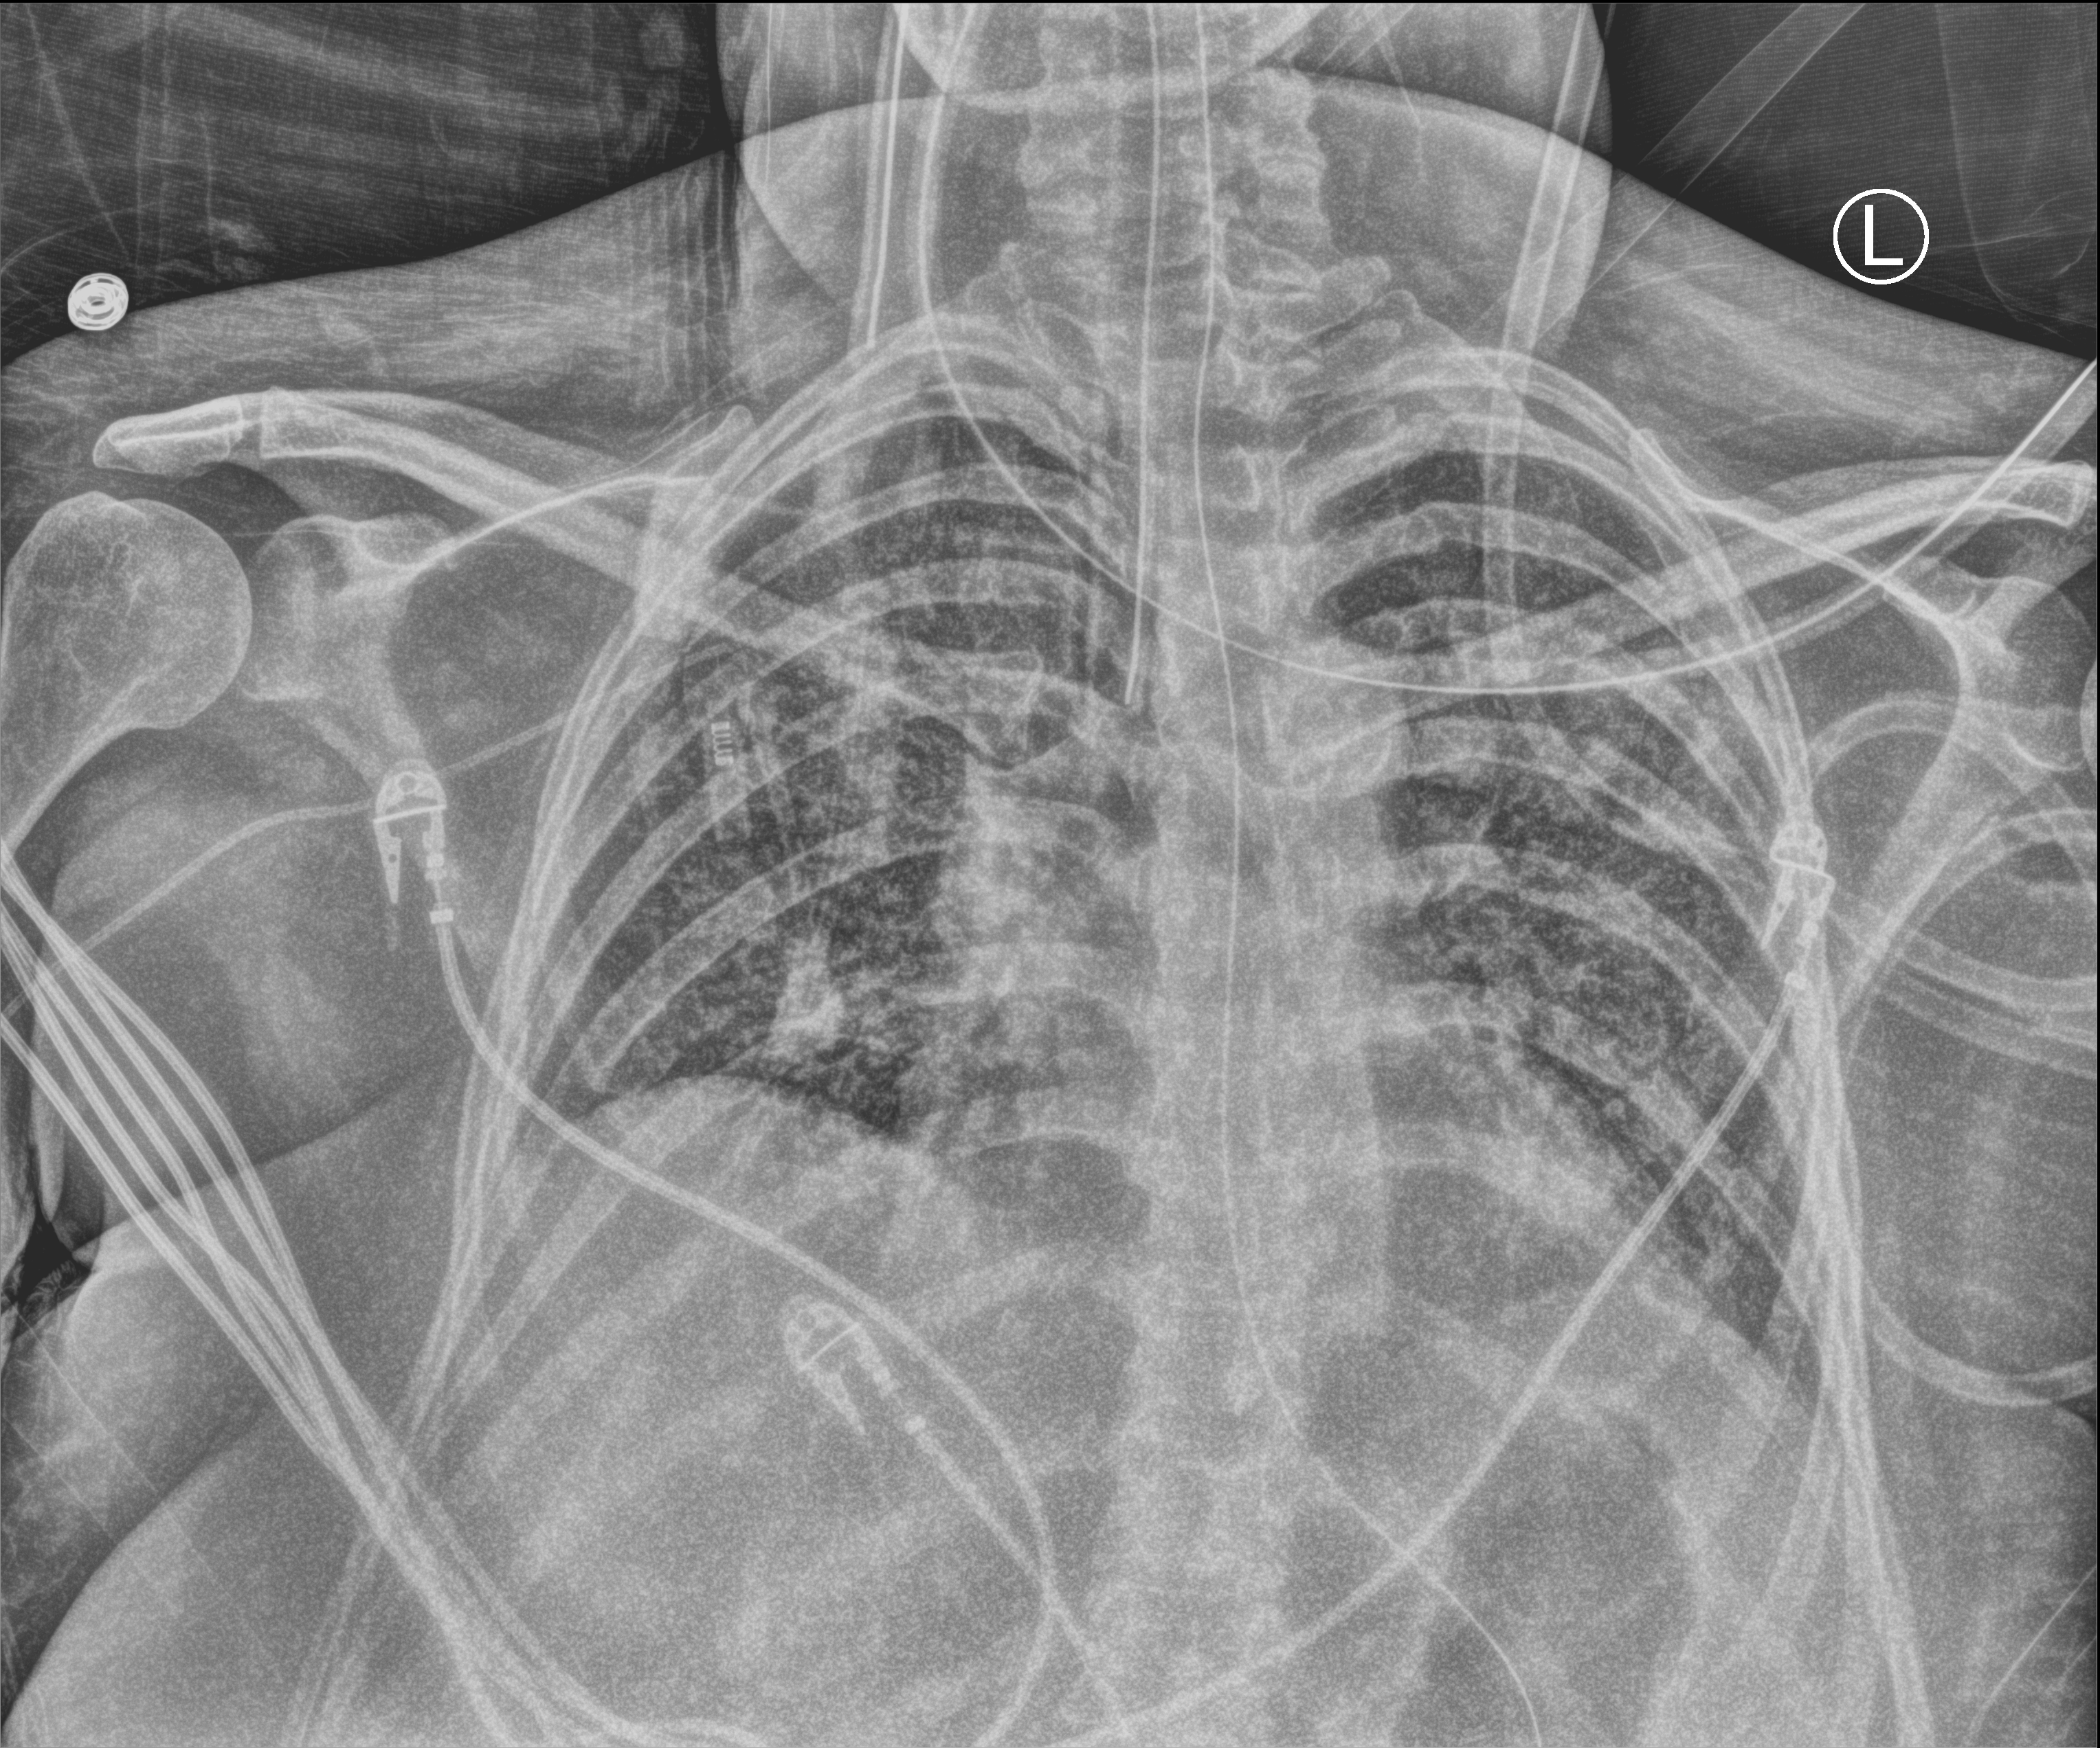
Bedside chest radiograph (computed radiography), anteroposterior (AP) projection. Patient hospitalised with COVID-19; female, aged 18–59 years.
Admission-level facts for this patient (not findings on this image; timing relative to this image not recorded): chronic kidney disease (admission record): no; mechanically ventilated during this hospital stay: yes.